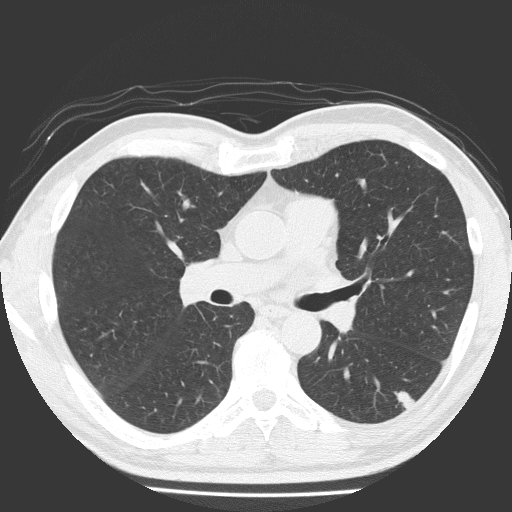
Low-dose screening chest CT, one axial slice; position 105 of 184 along the scan axis; reconstruction kernel FC51; 120 kVp; lung window (W 1500 / L -600 HU); 512 × 512 image matrix.
Outlined on this slice (expert manual segmentation):
- lesion 1 (tumor, lower lobe of left lung): bounding box <394,391,415,409> (left, top, right, bottom; pixels)